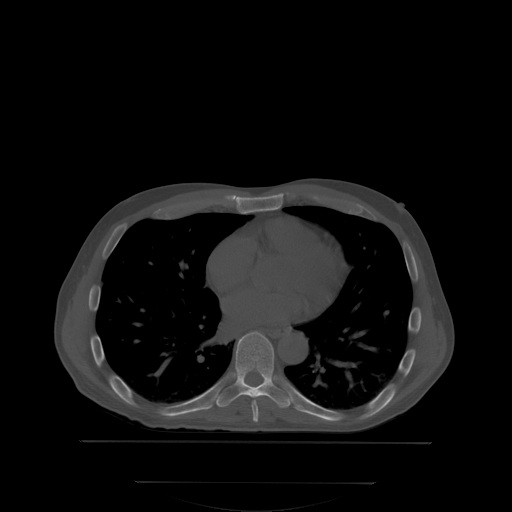
CT including the spine, one axial slice; bone window (W 1800 / L 400 HU); 2.5 mm slice thickness; 512 × 512 image matrix, field of view 500 × 500 mm. Male patient, age 58 years. Case-level facts recorded for this patient, not image findings: primary cancer: prostate; vertebrae with lytic lesions (as recorded): L1.
Outlined on this slice (semi-automatically segmented with operator editing):
- T7 vertebra: box from (x=251, y=400) to (x=259, y=420) px
- T8 vertebra: (x=216, y=331)–(x=290, y=407)